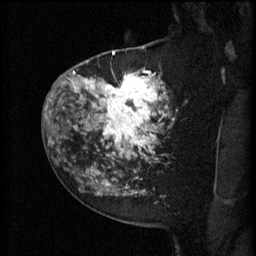
Breast MRI (dynamic contrast-enhanced), one sagittal slice; position 43 of 60 along the scan axis; 3 images stored at this slice position (order not interpretable as contrast timing); 1.5 T; TE 4.2 ms, TR 11 ms; 2 mm slice thickness; 256 × 256 image matrix, field of view 180 × 180 mm. Patient: female, 52 years.
Annotated regions visible in this slice (semi-automatically segmented with operator editing):
- analysis volume of interest (the breast-tissue region the enhancement analysis was run in; not a lesion): box from (x=81, y=52) to (x=174, y=157) px
- tumour enhancement mask (voxels above the 70 % enhancement threshold inside the analysis volume of interest): (x=81, y=52)–(x=174, y=157)